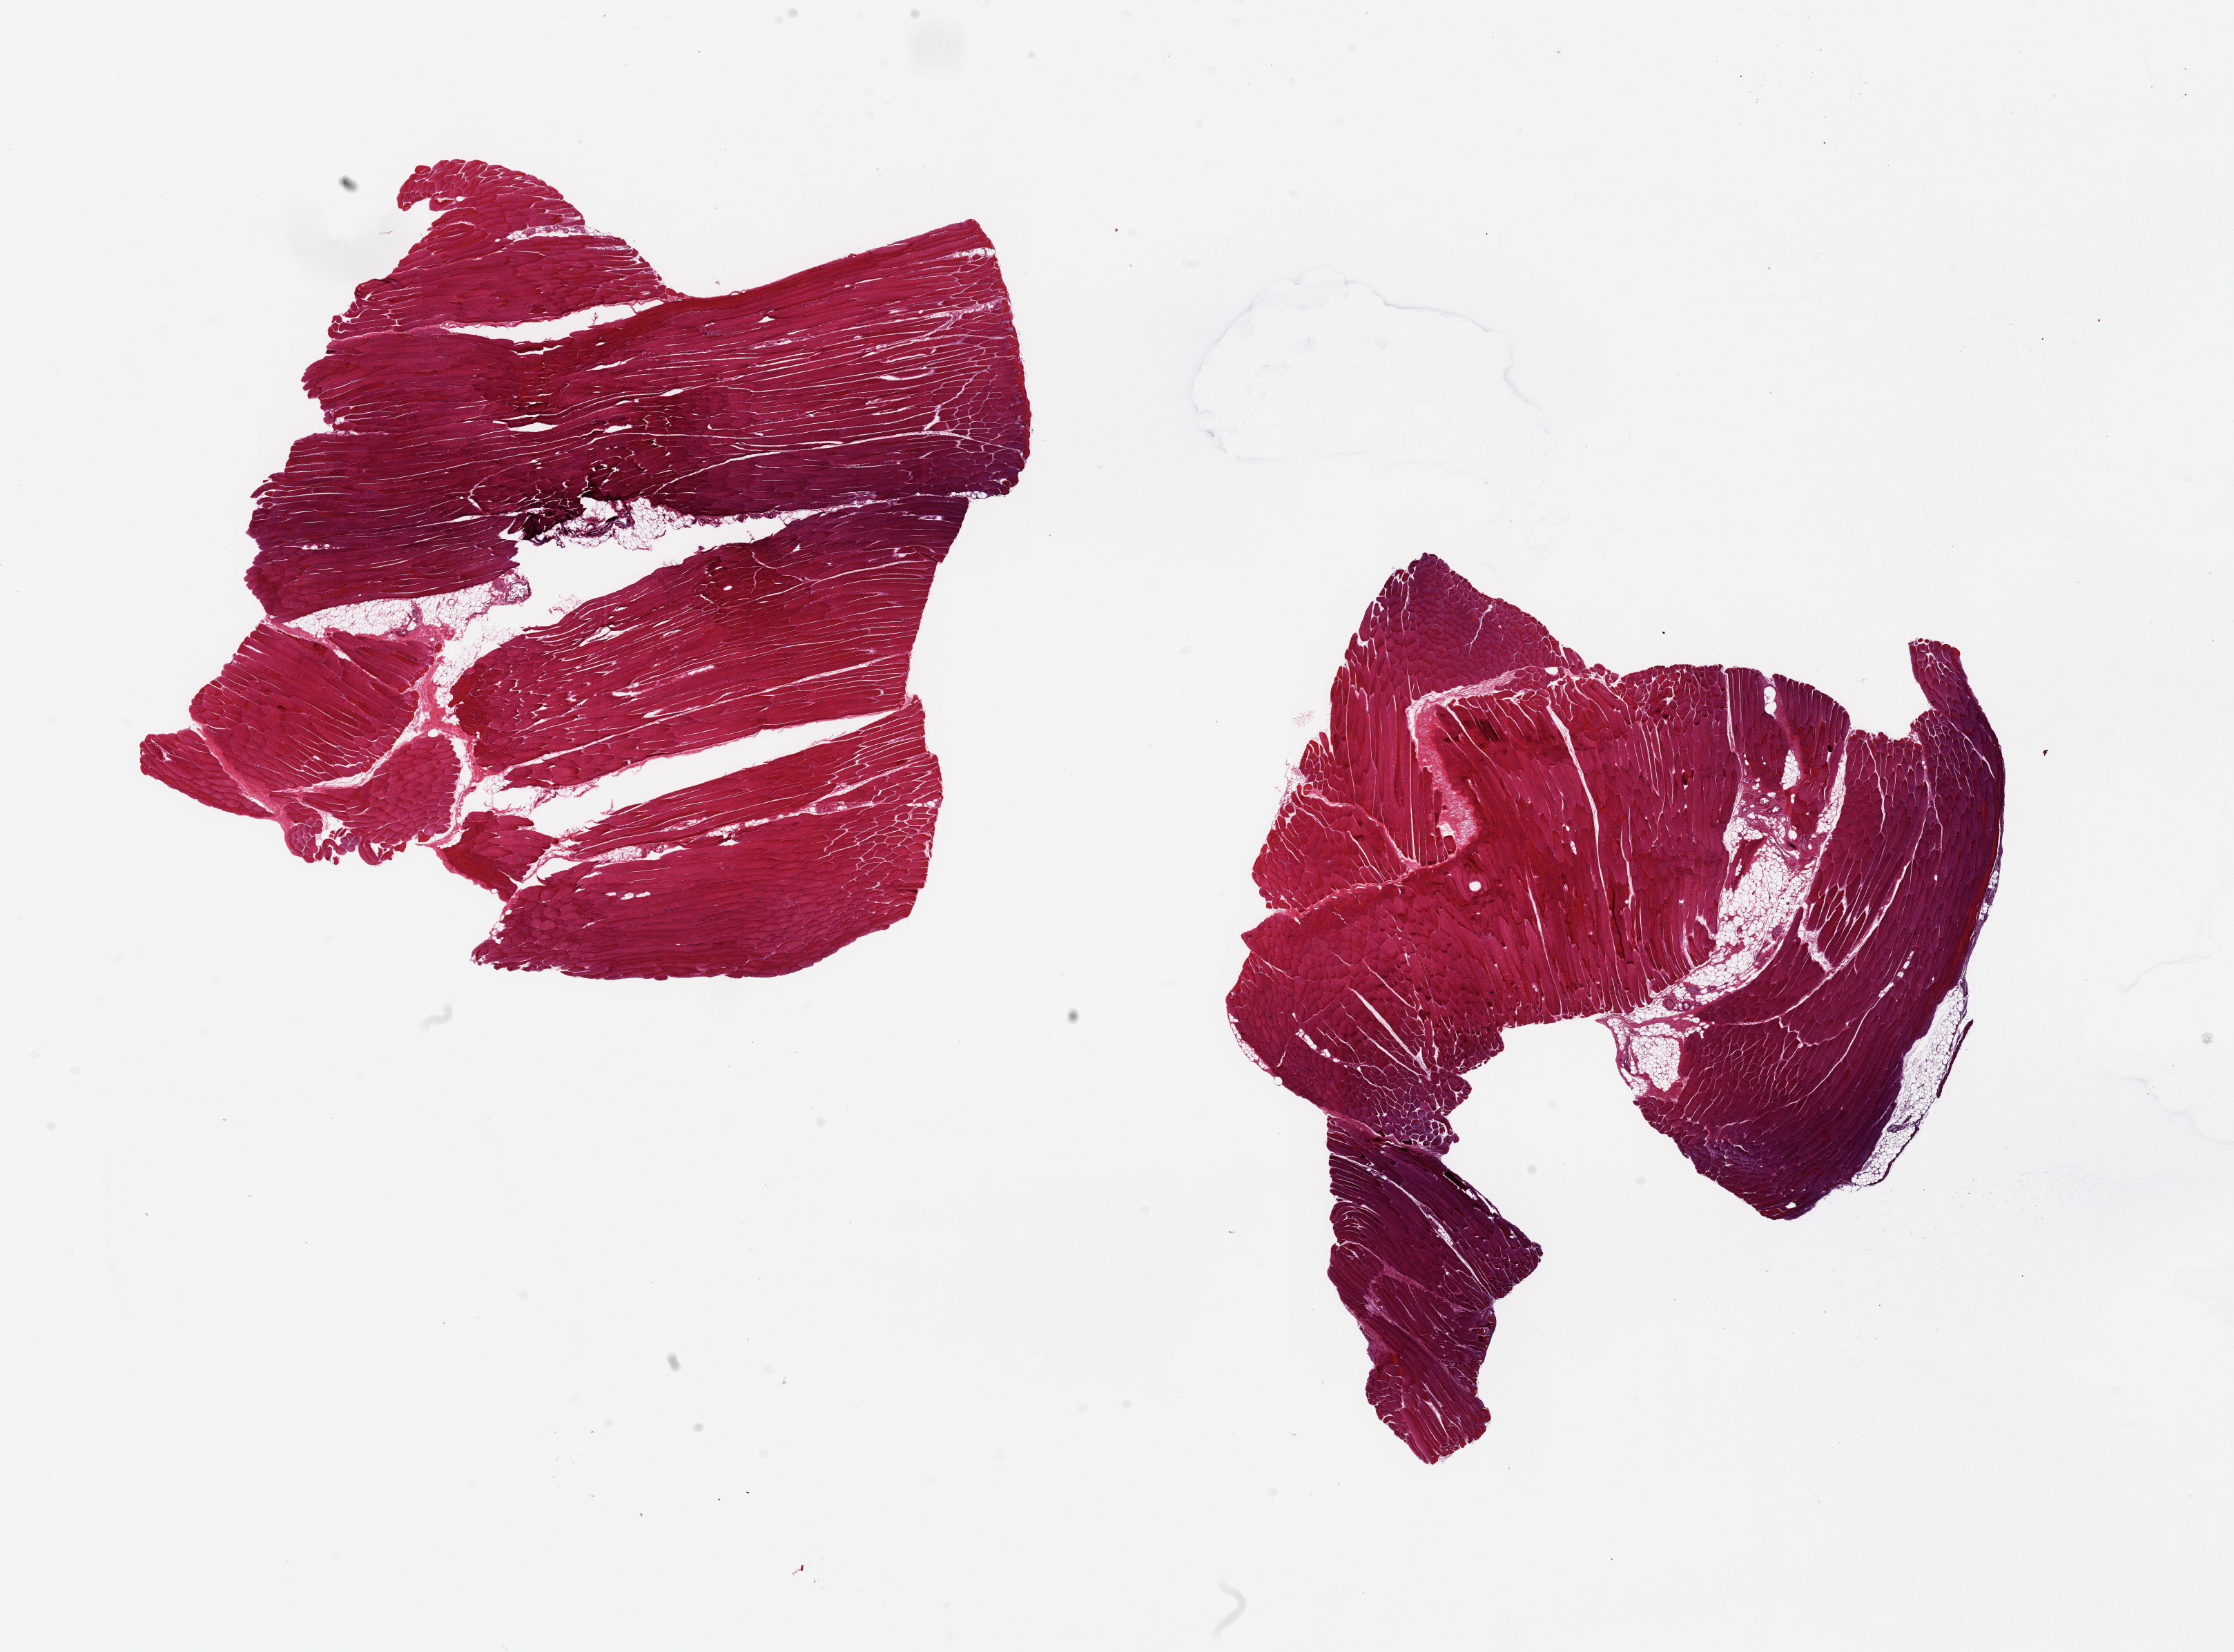
Whole-slide image, H&E stain, a low-resolution overview of the entire scanned area, about 25.6 x 18.9 mm. PAXgene-fixed paraffin-embedded (PFPE) section. Sampled site (target tissue): skeletal muscle. Tissue donor sample. Male donor.
Pathologist's review note for this sample: 2 pieces, 10x9.5 & 10x9mm; 10% adipose within specimen.